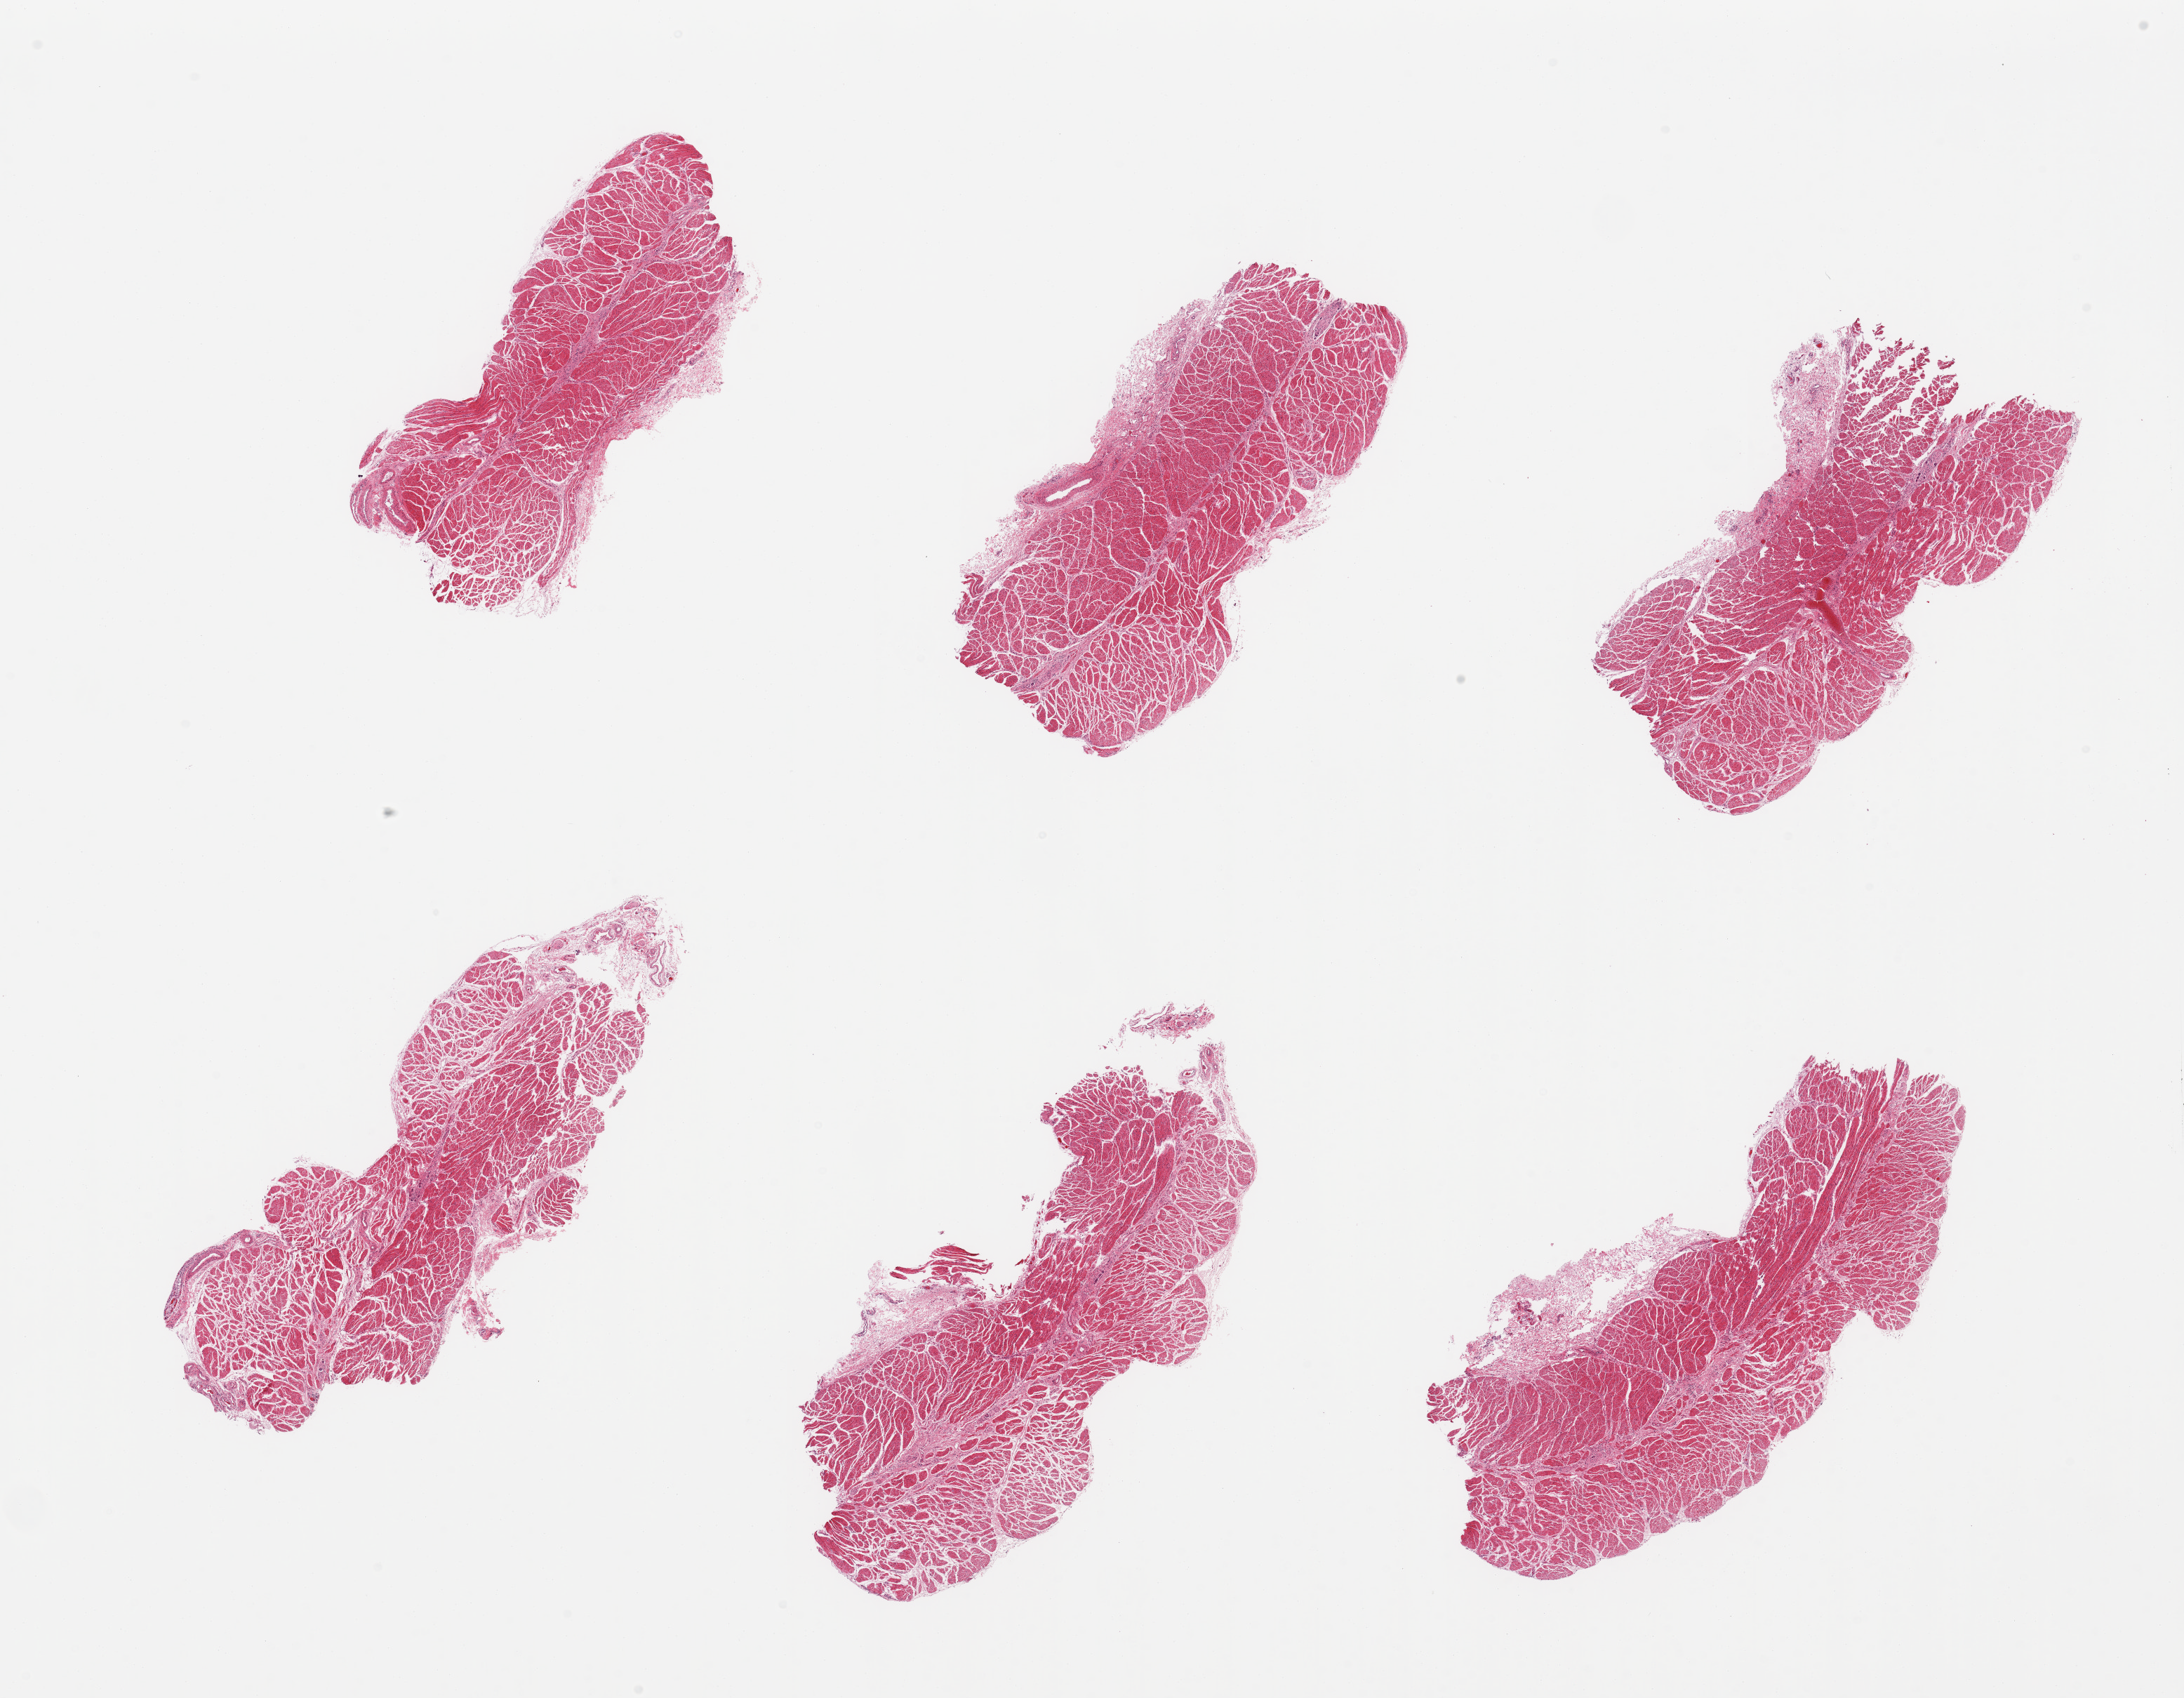
H&E whole-slide image — a low-resolution overview of the entire scanned area, about 24.6 x 19.1 mm. PAXgene-fixed, paraffin-embedded tissue. Section of gastroesophageal junction (target tissue). Tissue donor sample. Male donor.
Reviewer comment on this tissue sample: 6 pieces; focal submucosal stroma present.